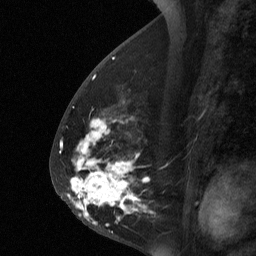
Breast MRI (dynamic contrast-enhanced), one sagittal slice; slice 29 of 64 in the series (ordered by position); dynamic contrast-enhanced study with each time point stored as its own series, time point 2 of 3 at this slice position (early post-contrast, ordered by acquisition time); 1.5 T; TE 4.8 ms, TR 27 ms; 2 mm slice thickness; 256 × 256 image matrix, field of view 180 × 180 mm. Female patient, age 56 years. From the clinical record (not read from this slice): setting: breast cancer imaged before/during neoadjuvant chemotherapy; receptor status: HER2-positive.
Outlined on this slice (semi-automatically segmented with operator editing):
- analysis volume of interest (the breast-tissue region the enhancement analysis was run in; not a lesion): box from (x=59, y=104) to (x=153, y=229) px
- tumour enhancement mask (voxels above the 90 % enhancement threshold inside the analysis volume of interest): (x=68, y=145)–(x=137, y=224)